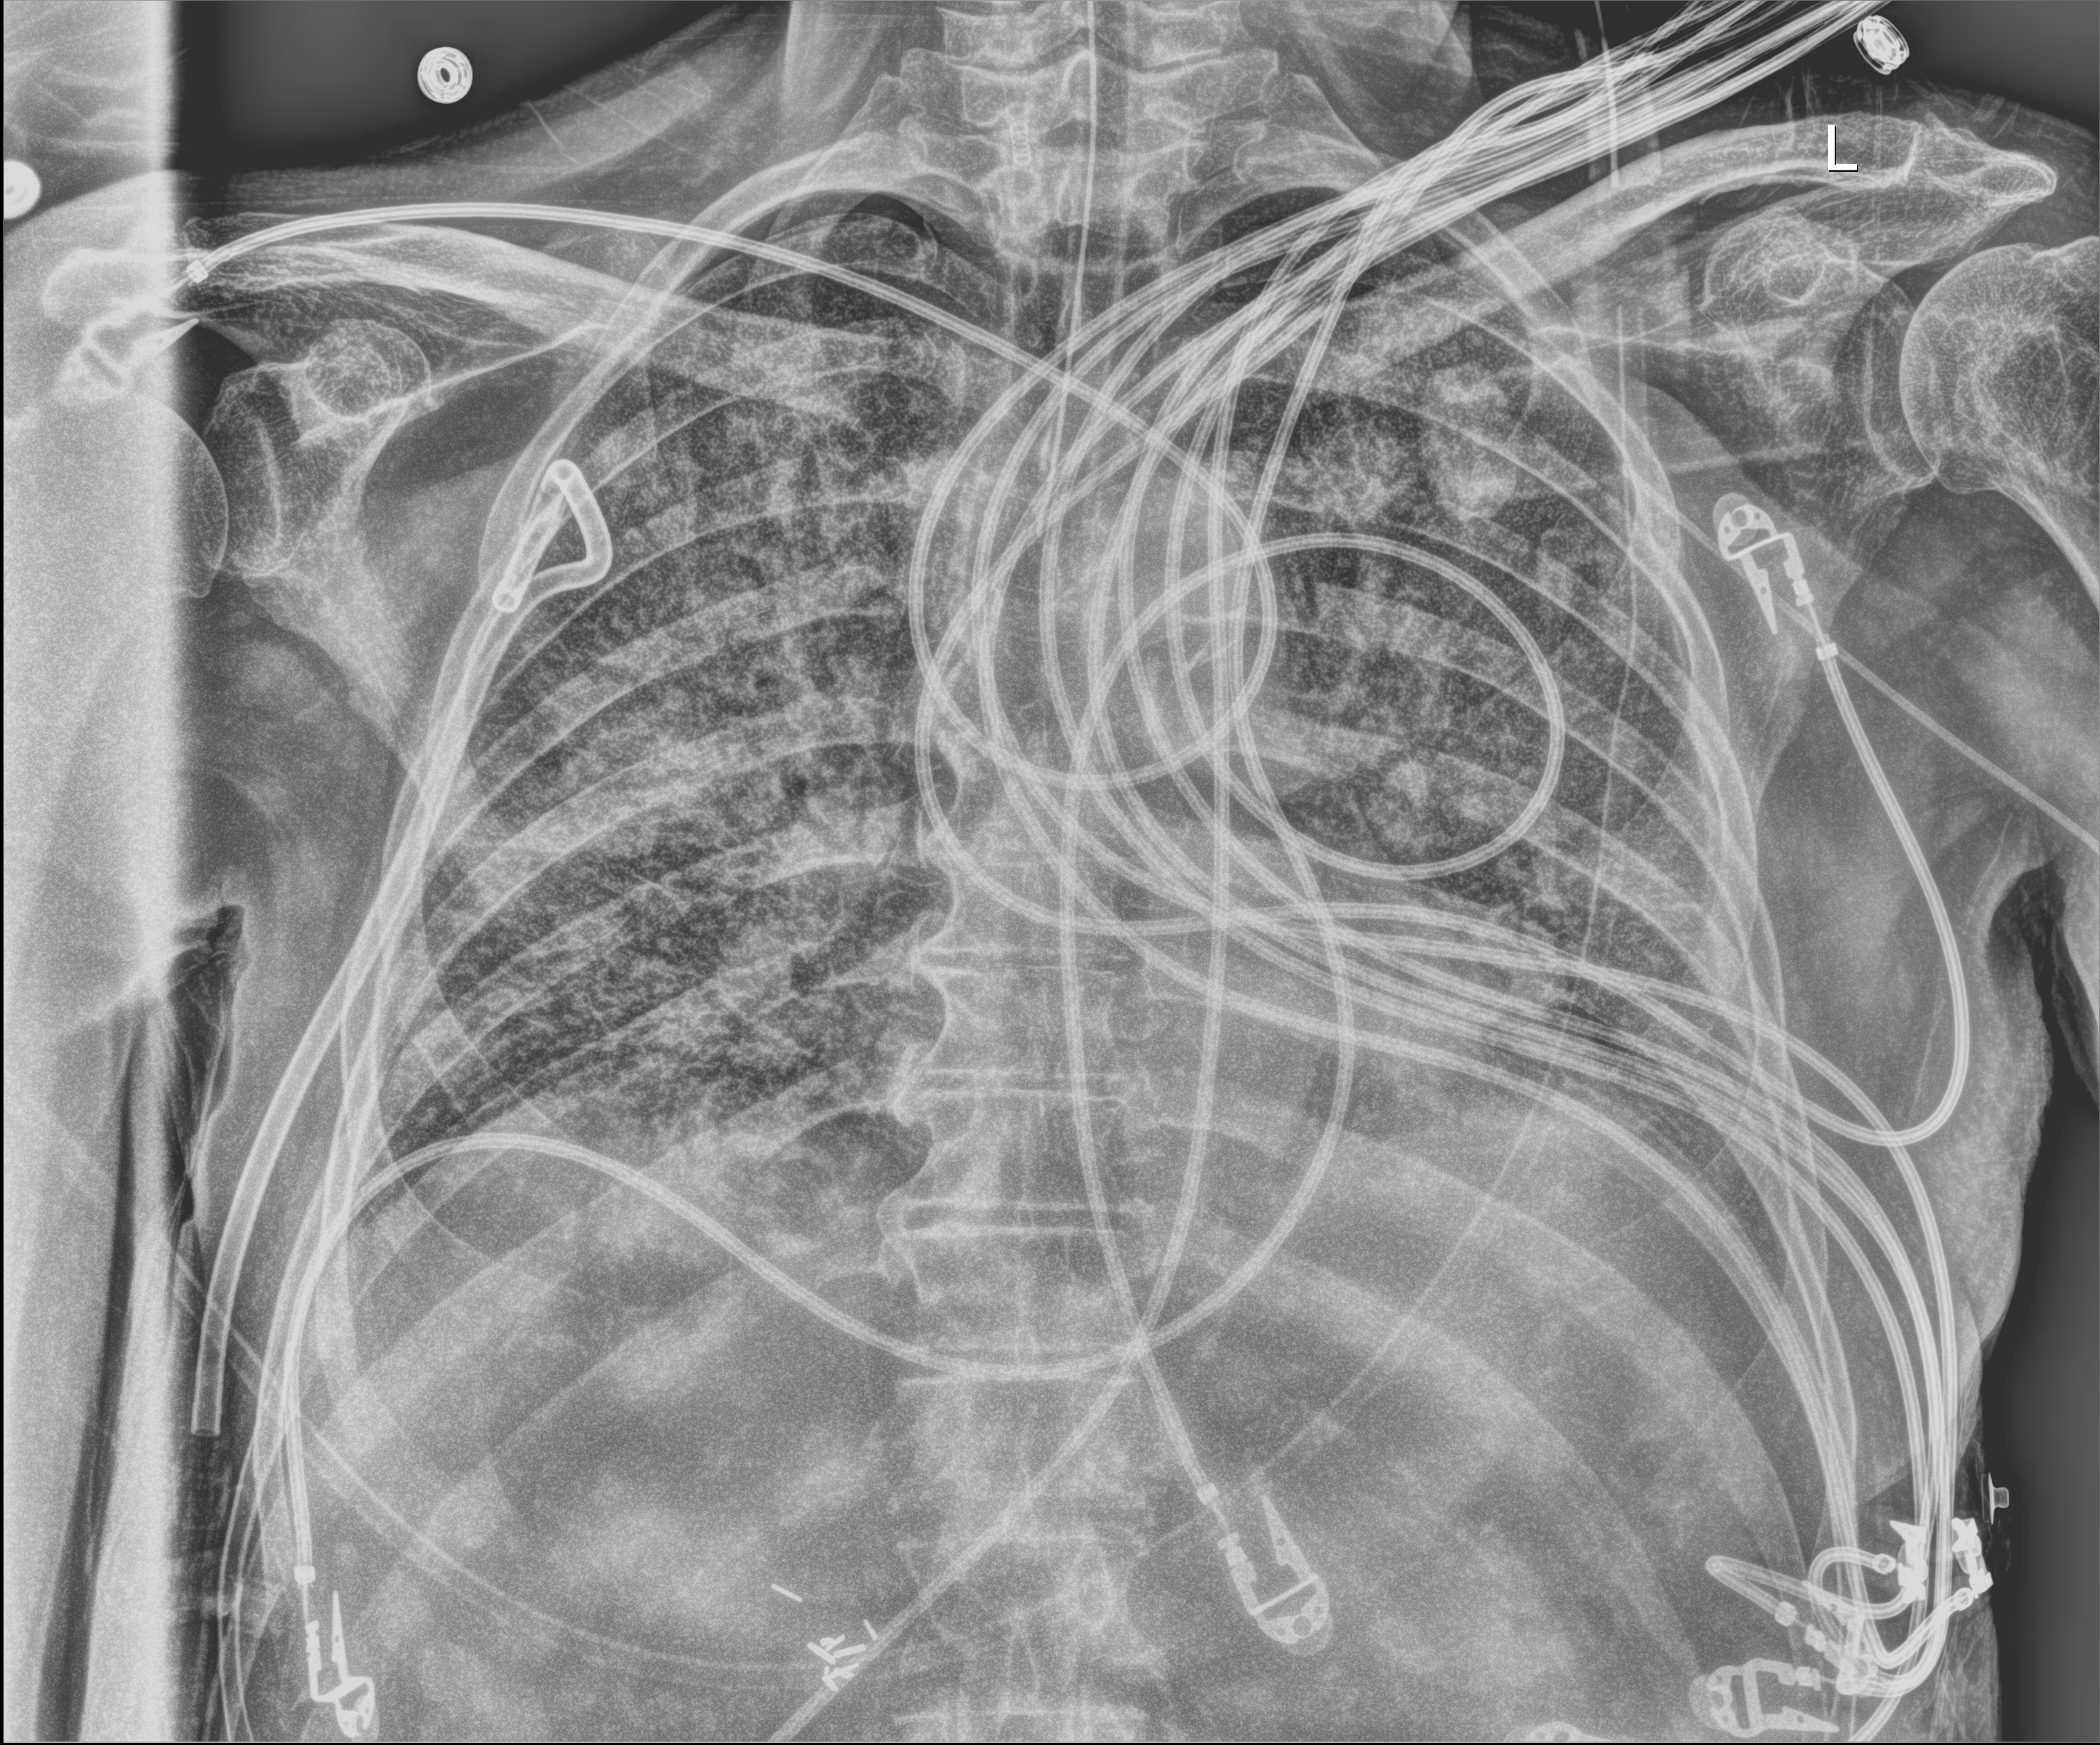
Portable chest radiograph, anteroposterior (AP) projection. Male patient hospitalised with COVID-19, age 75–90 years.
Hospital-stay facts (about this admission, not read from this image; timing relative to this image not recorded):
- admitted to intensive care during this hospital stay: yes
- smoking status (admission record): never
- chronic kidney disease (admission record): no